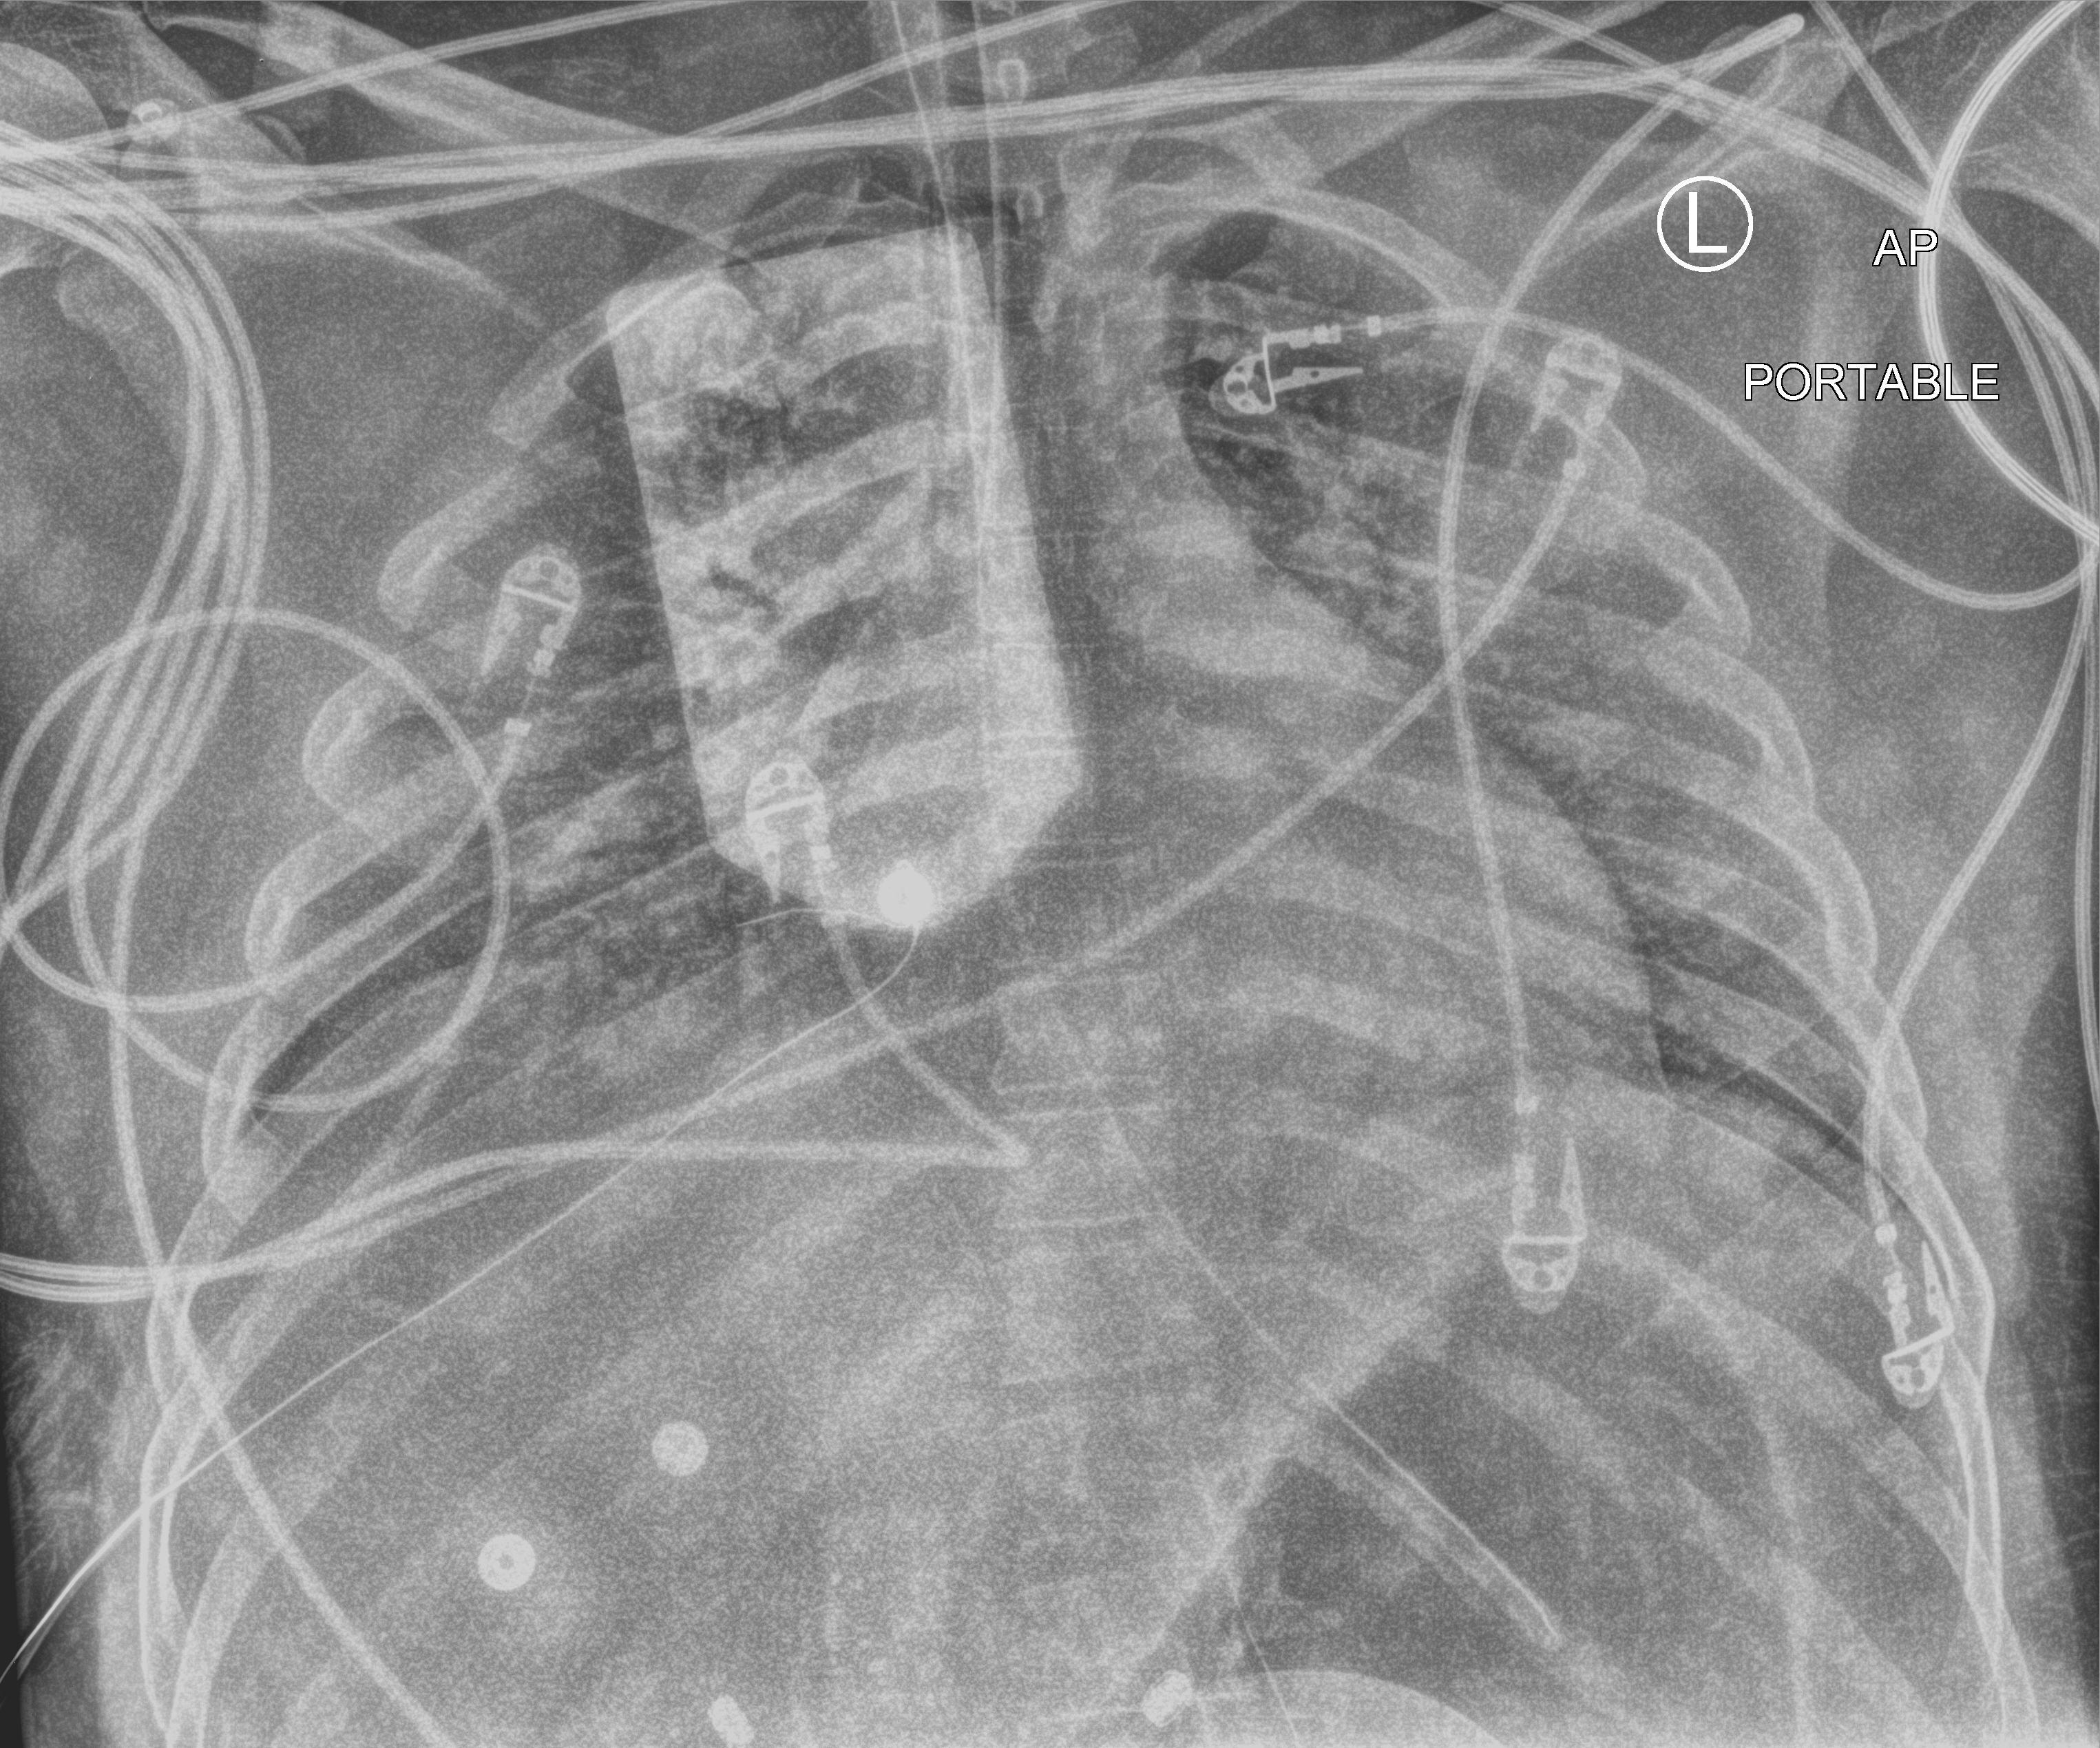
Chest X-ray (portable), anteroposterior (AP) projection. Patient hospitalised with COVID-19, aged 18–59 years.
Admission-level facts for this patient (not findings on this image; timing relative to this image not recorded): admitted to intensive care during this hospital stay: yes; mechanically ventilated during this hospital stay: yes.